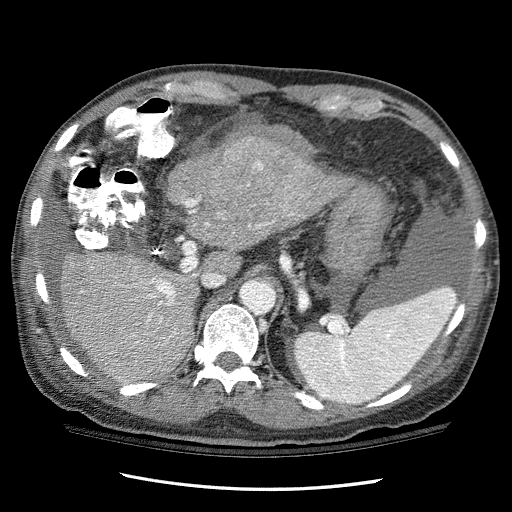
Contrast-enhanced abdominal CT (liver protocol), one axial slice. Position 72 of 114 along the scan axis. One of 3 acquisitions stored at this slice position. Soft-tissue window (W 400 / L 40 HU). 2.5 mm slice thickness. 512 × 512 image matrix. From the clinical record (not read from this slice): diagnosis: hepatocellular carcinoma (patient treated with transarterial chemoembolisation; whether this scan precedes or follows treatment is not stated here); TNM stage (as recorded): Stage-I; Child-Pugh class: C; tumour differentiation: well differentiated; tumour nodularity: uninodular.
Outlined on this slice (semi-automatic segmentation, software-assisted and operator-edited):
- liver parenchyma outside the tumour (the mass and vessels are separate outlines, so this box may not span the whole liver): bounding box [x1, y1, x2, y2] px = [60, 150, 359, 384]
- mass: [221, 121, 318, 192]
- liver vessels: [81, 199, 274, 343]